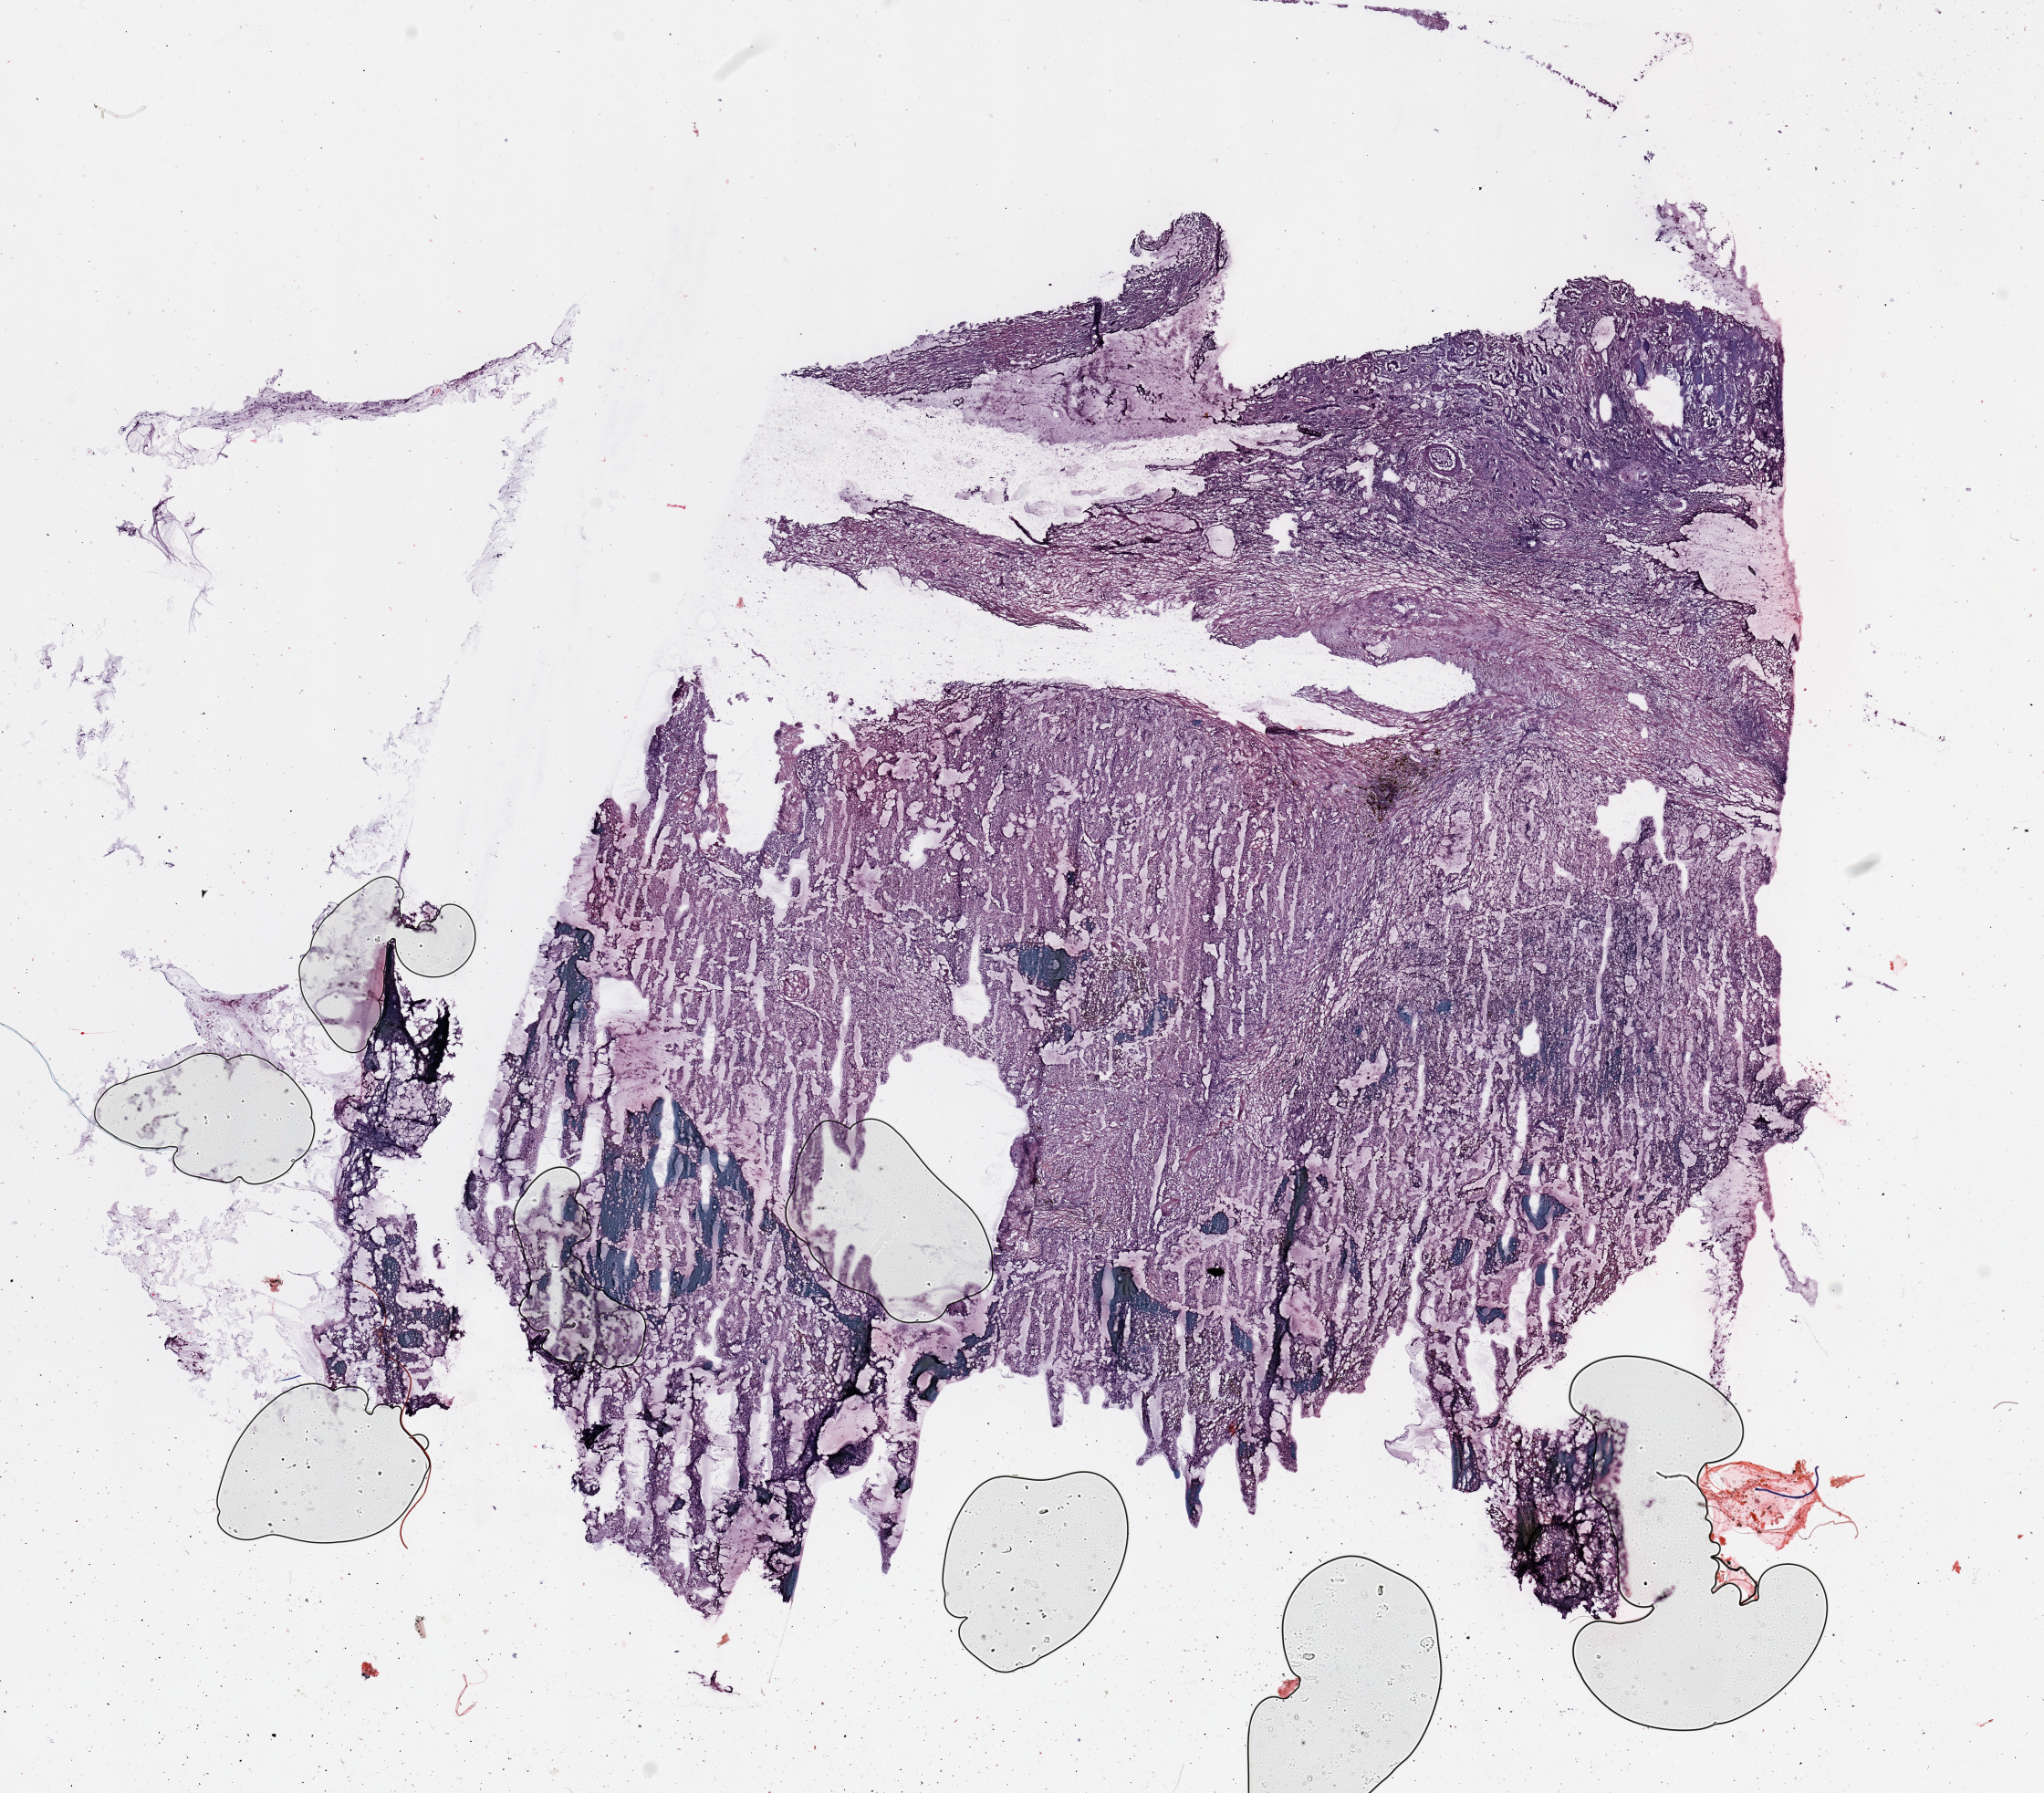
H&E whole-slide image — a low-resolution overview of the entire scanned area, about 17.7 x 15.5 mm (slide scanned at 20x), kidney, tumour tissue. Female, 57 y/o. Histologic grade: G2 (moderately differentiated).
- diagnosis: Renal cell carcinoma, NOS
- primary tumour site (as recorded): upper pole
- AJCC pathologic stage: I